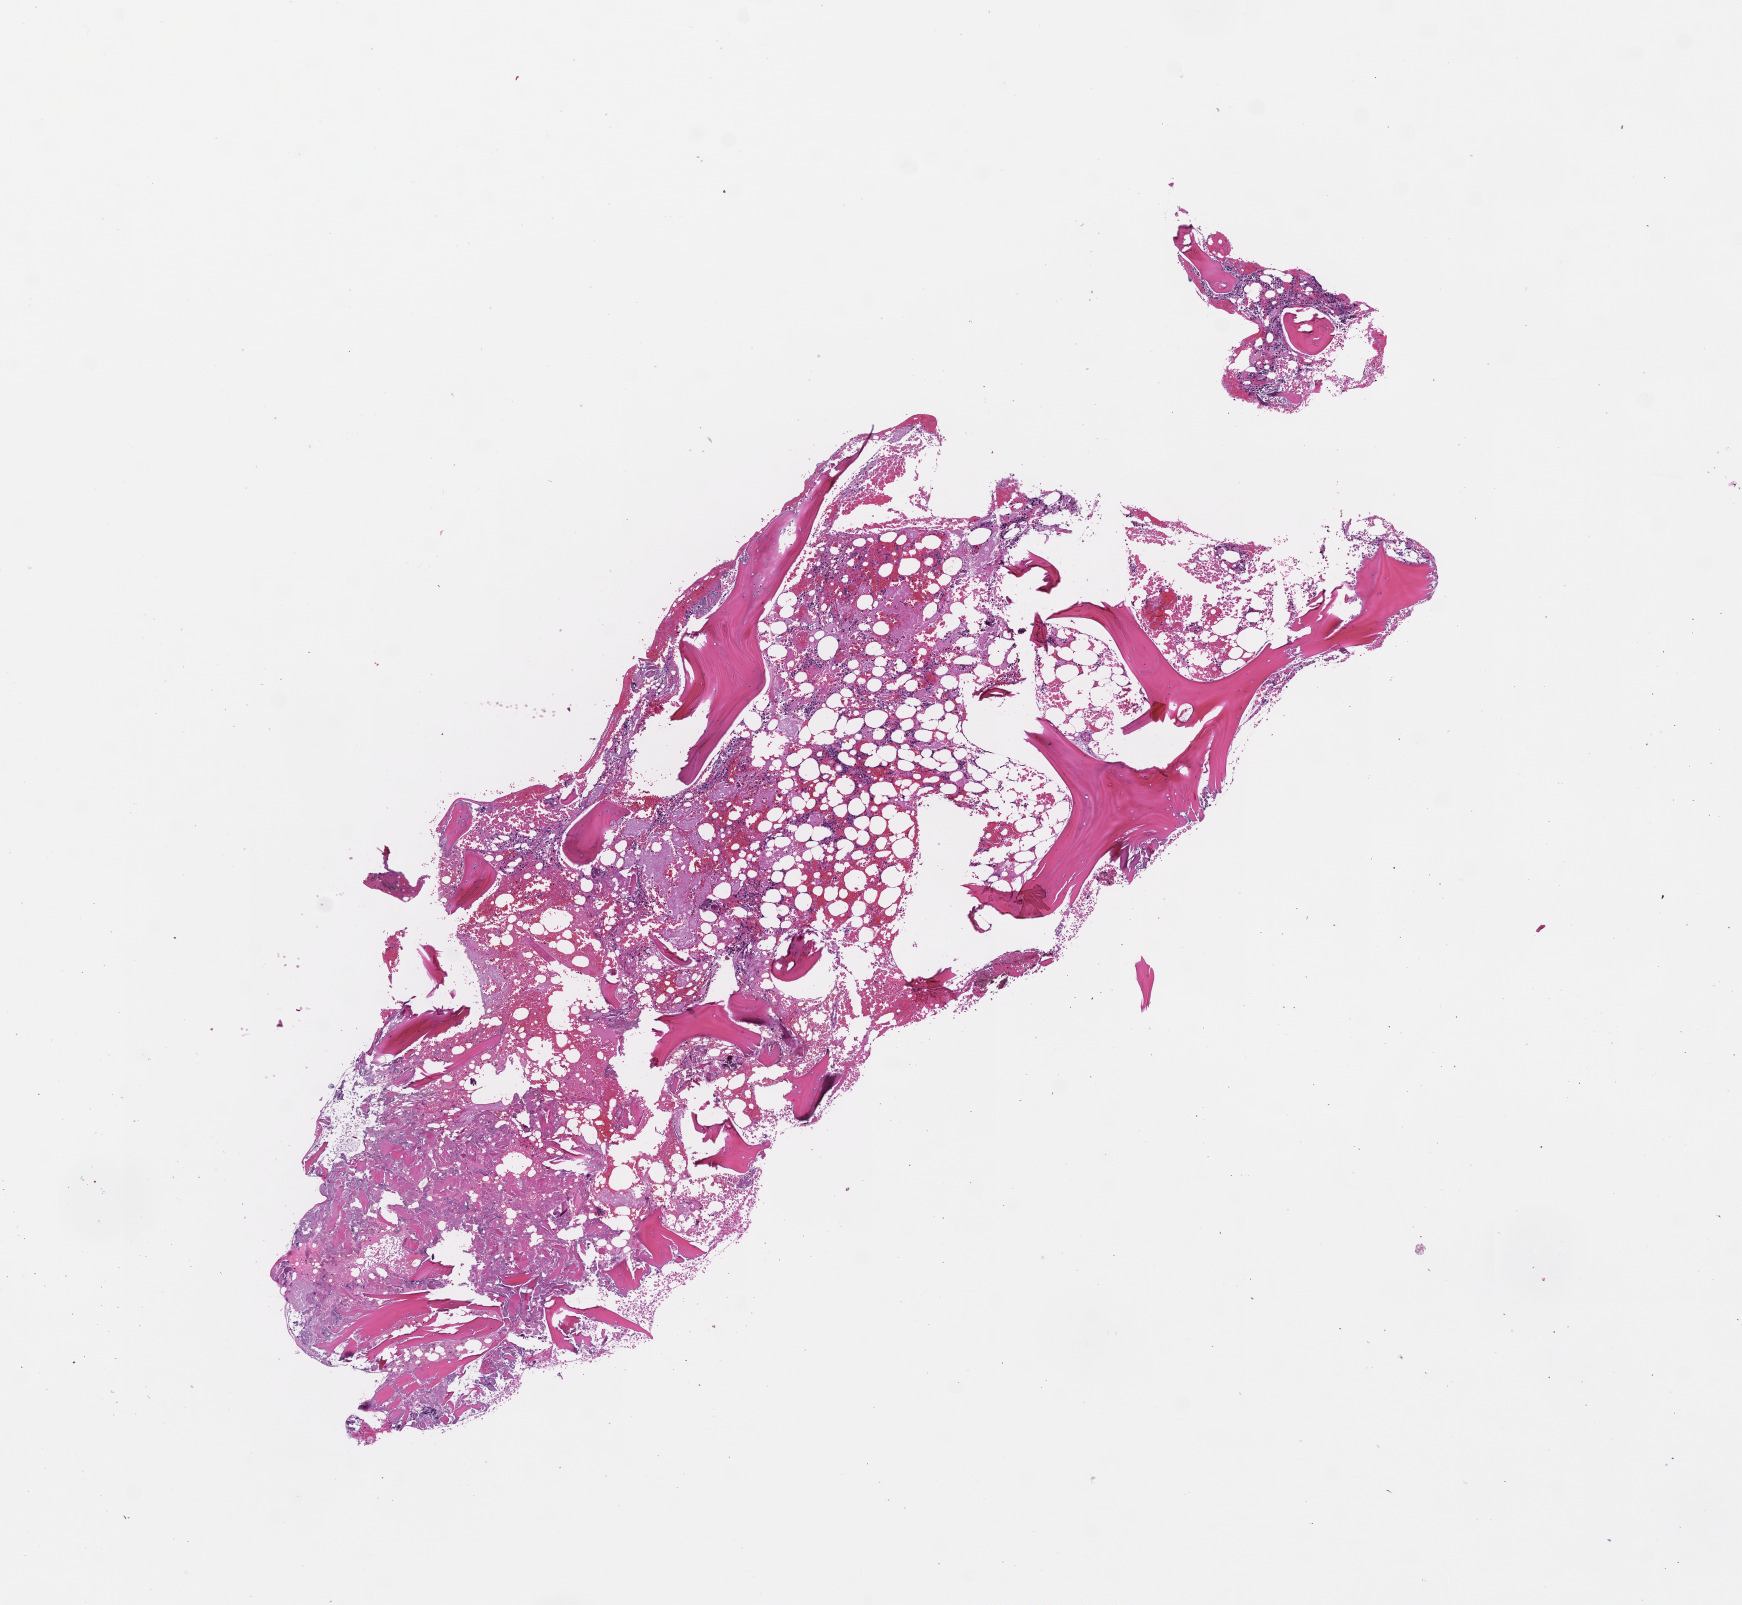
Haematoxylin and eosin whole-slide image — whole scanned area (about 7.0 x 6.5 mm) shown as a low-resolution overview. Formalin-fixed paraffin-embedded section. Site: bone marrow. Collected at baseline (before treatment). Patient: male.
- from a patient with: Plasma Cell Myeloma